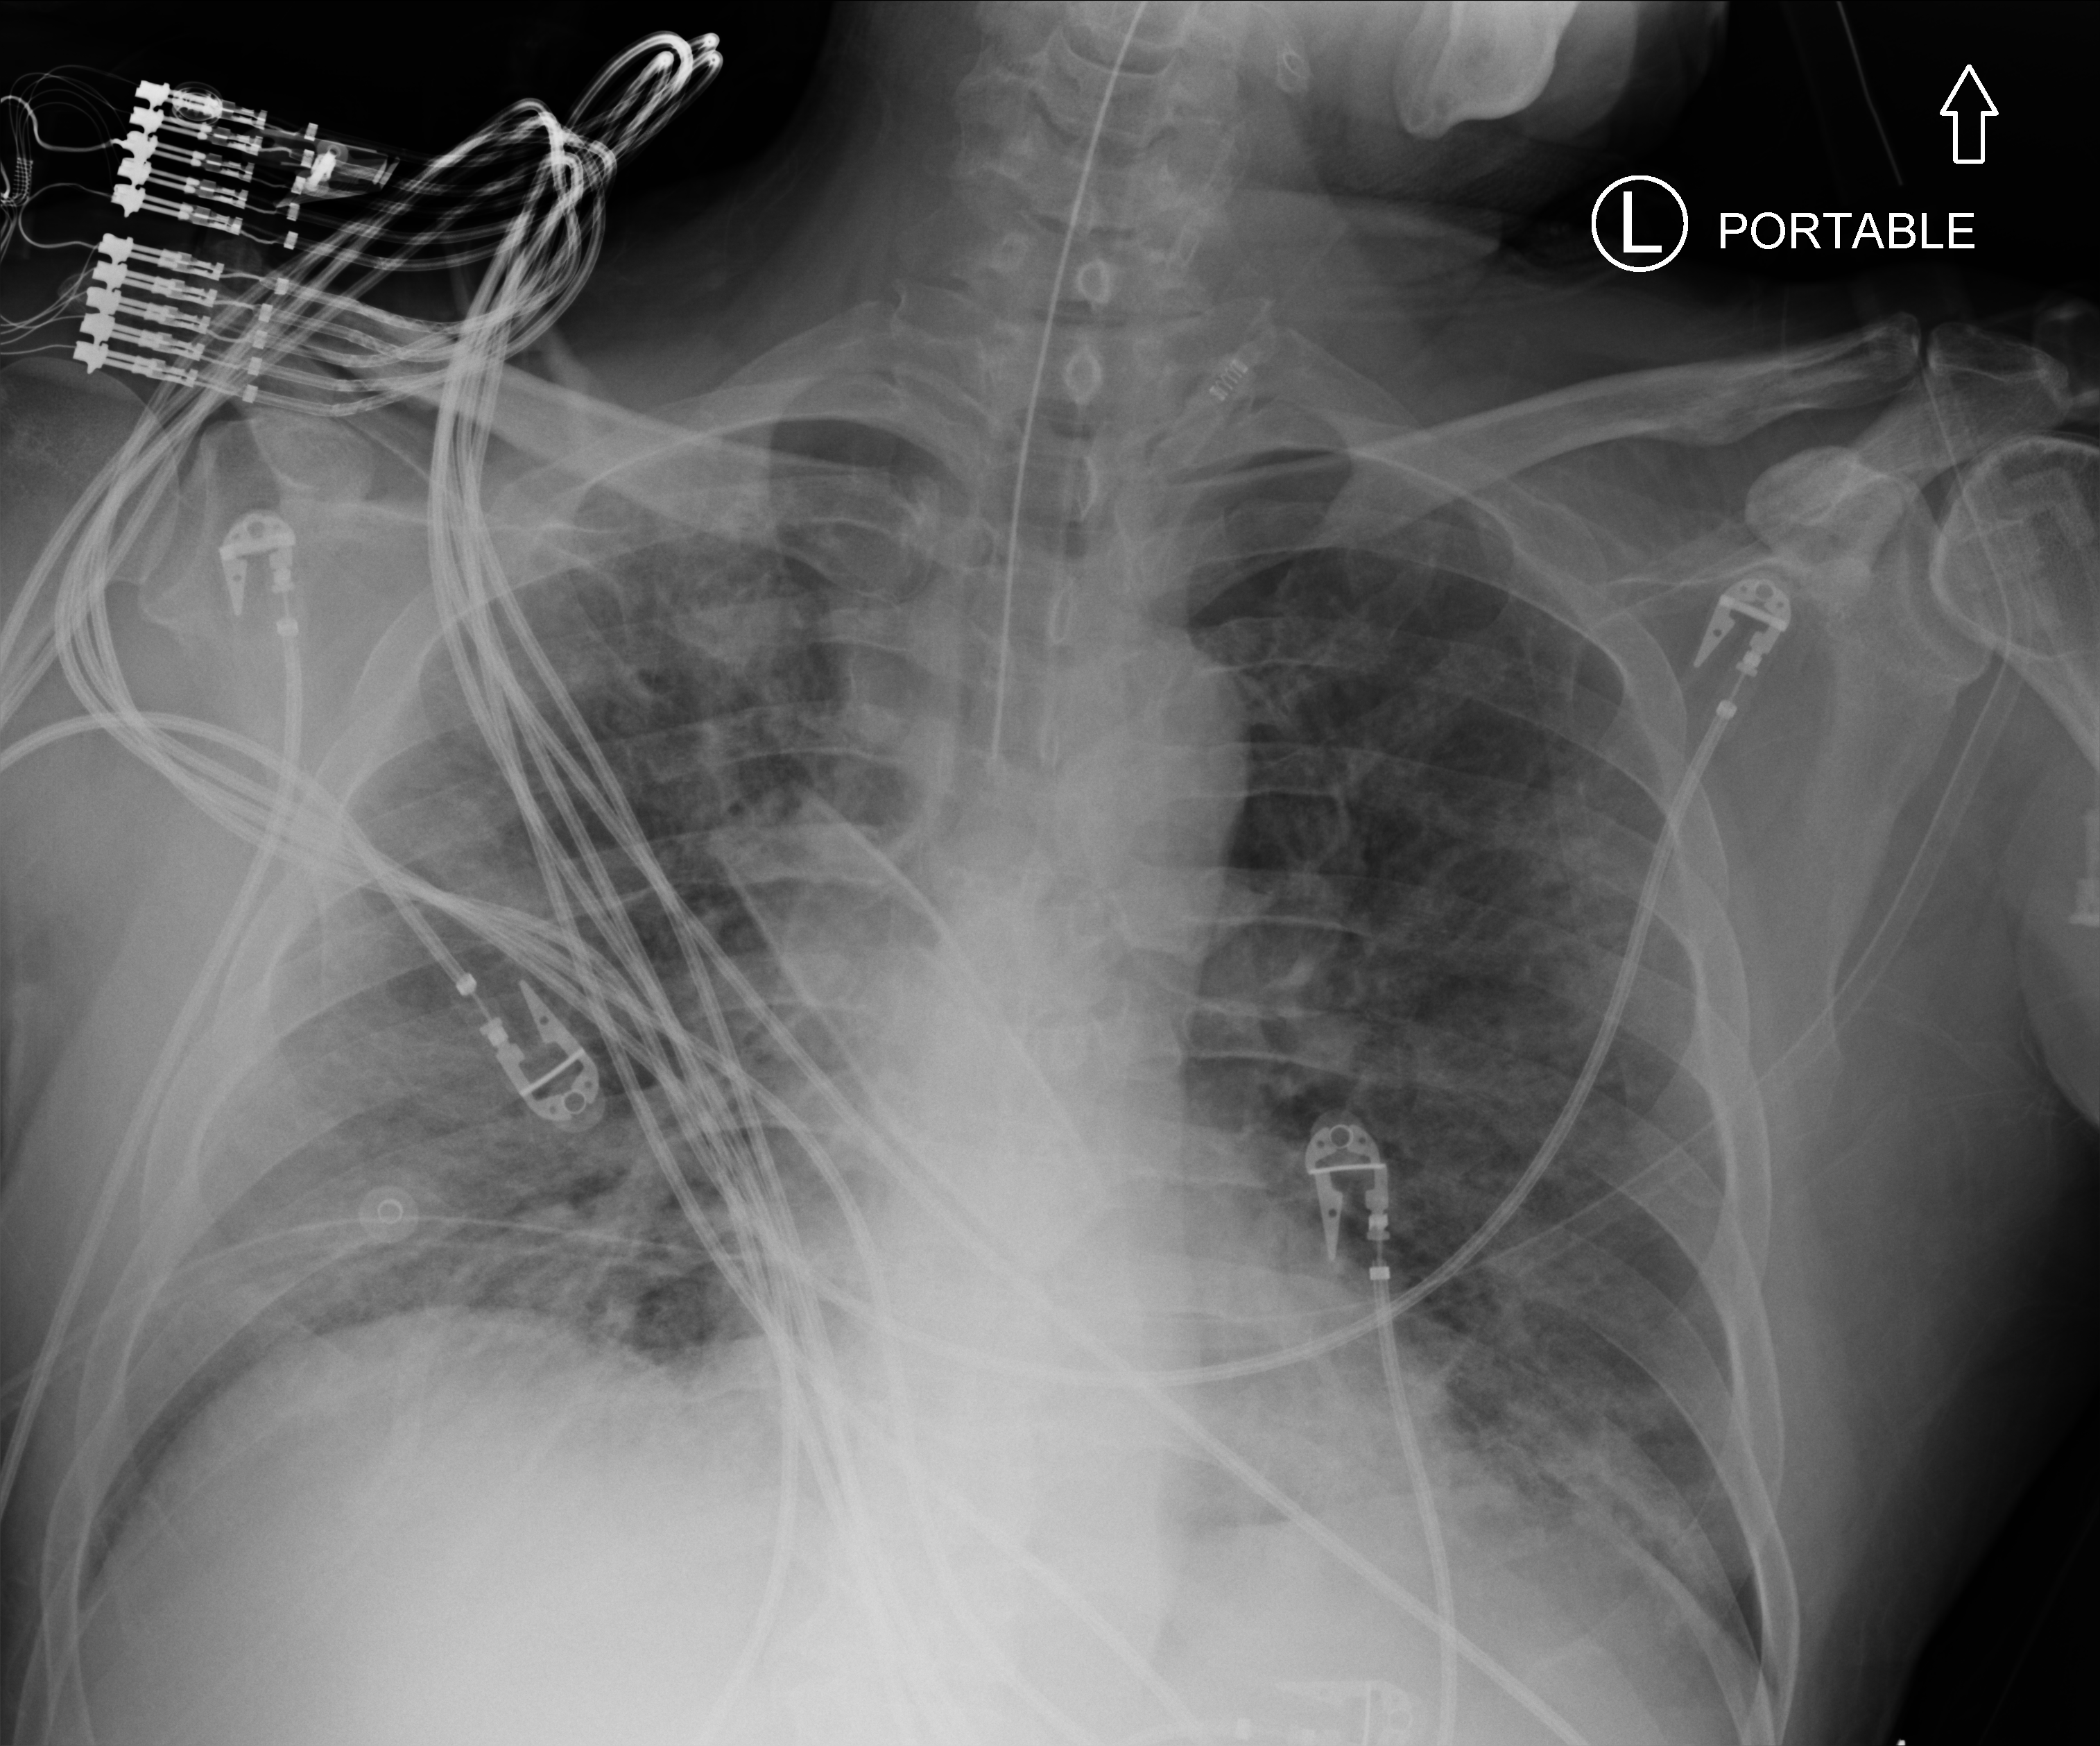
Bedside chest radiograph (computed radiography). Male patient hospitalised with COVID-19, age 18–59 years.
Admission-level facts for this patient (not findings on this image; timing relative to this image not recorded):
- COPD (admission record): no
- smoking status (admission record): former
- length of hospital stay: 40 days